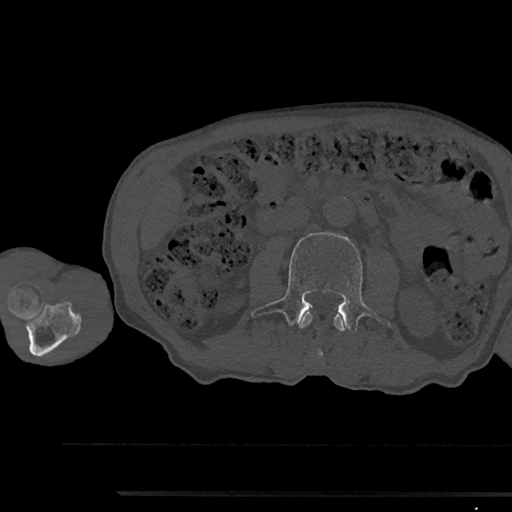
CT including the spine, one axial slice. Position 508 of 797 along the scan axis. 120 kVp. Bone window (W 1800 / L 400 HU). 0.5 mm slice thickness. 512 × 512 image matrix, field of view 367 × 367 mm. Patient: male, 79 years. Case-level facts recorded for this patient, not image findings: primary cancer: prostate.
Outlined on this slice (semi-automatic segmentation, software-assisted and operator-edited):
- L2 vertebra: bounding box (x1, y1, x2, y2) in pixels: (298, 313, 345, 357)
- L3 vertebra: (251, 233, 391, 330)